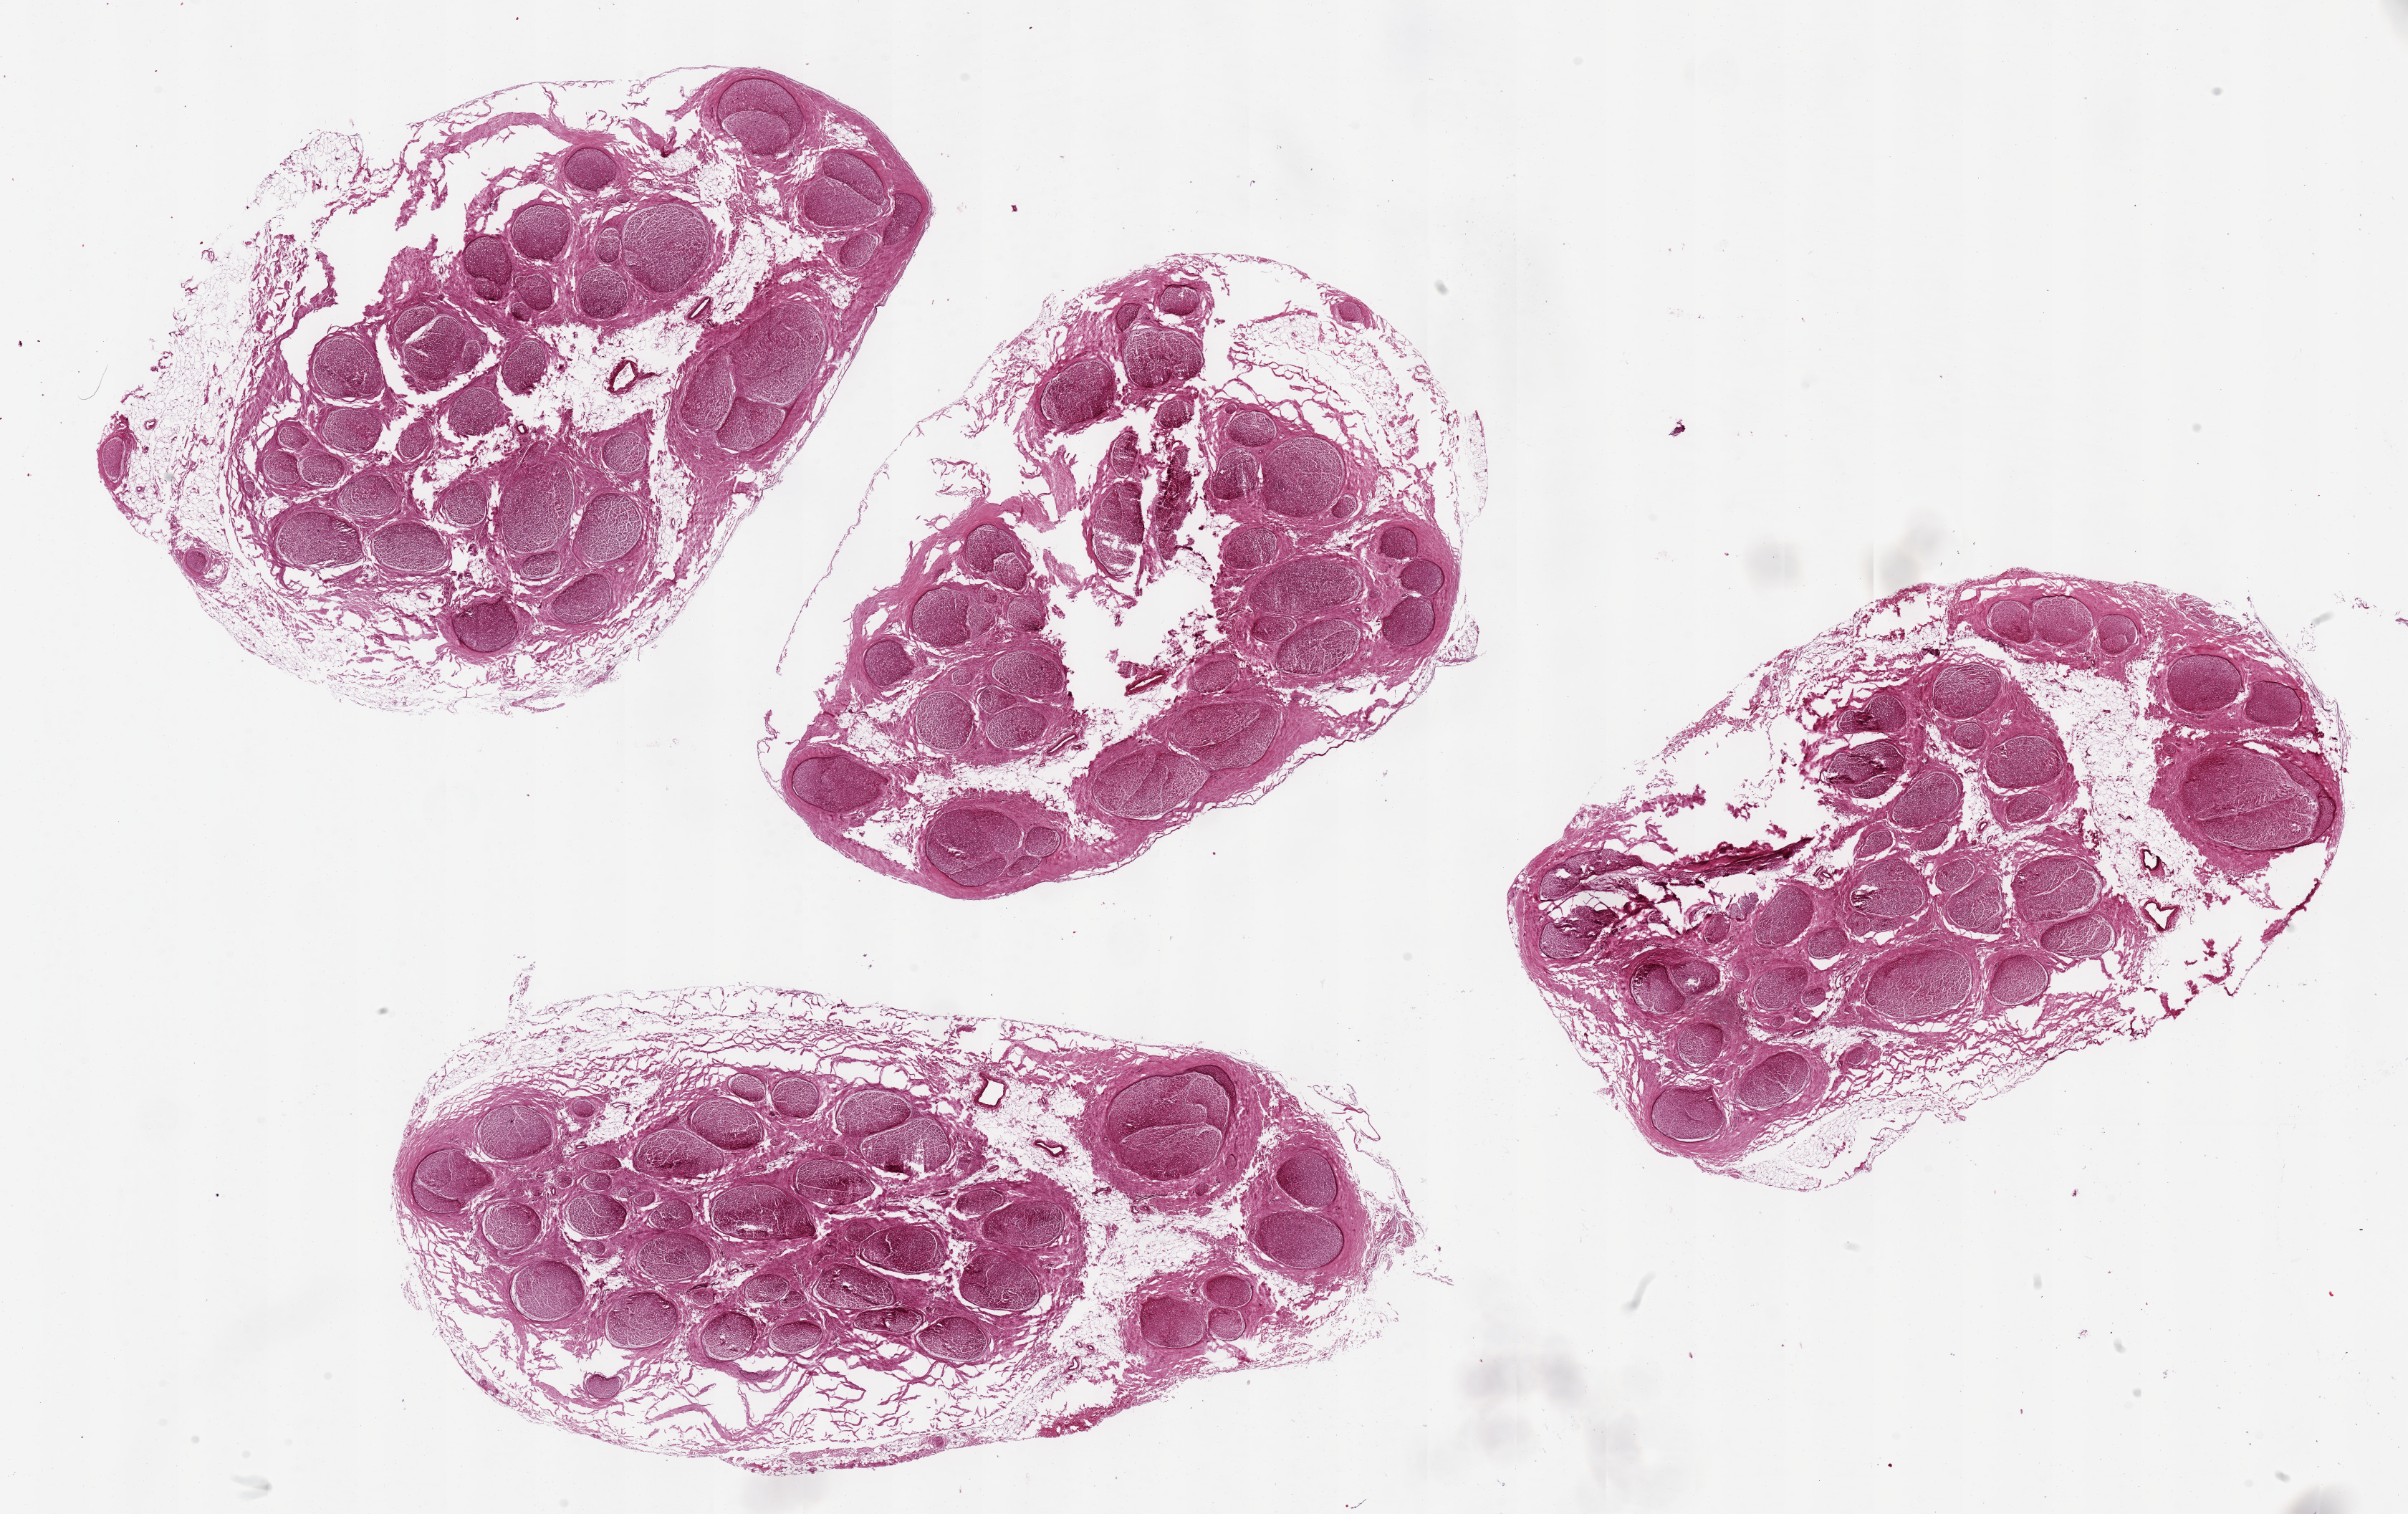
H&E whole-slide image, shown as a low-resolution overview of the whole scanned area (about 26.6 x 16.7 mm, acquisition: 20x scan), PAXgene-fixed, paraffin-embedded tissue, sampled site (target tissue): tibial nerve, tissue donor sample.
- review note (as recorded): 4 pieces up to 11x5 mm; ~30% adipose in and around nerve bundles